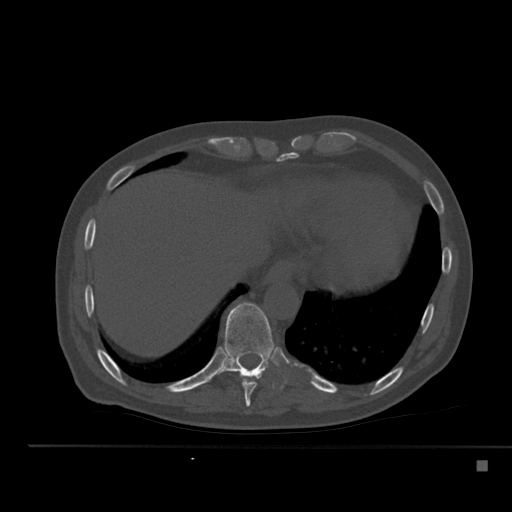
CT including the spine, one axial slice. Bone window (W 1800 / L 400 HU). 1.5 mm slice thickness. 512 × 512 image matrix, field of view 408 × 408 mm. Patient: male, 70 years. Case-level facts recorded for this patient, not image findings: primary cancer: renal; vertebrae with lytic lesions (as recorded): T4, T6, T10, T12, L3, L4, L5.
Annotated regions visible in this slice (semi-automatically segmented with operator editing):
- T10 vertebra: bounding box [x1, y1, x2, y2] px = [224, 302, 276, 377]
- T9 vertebra: [242, 373, 262, 407]